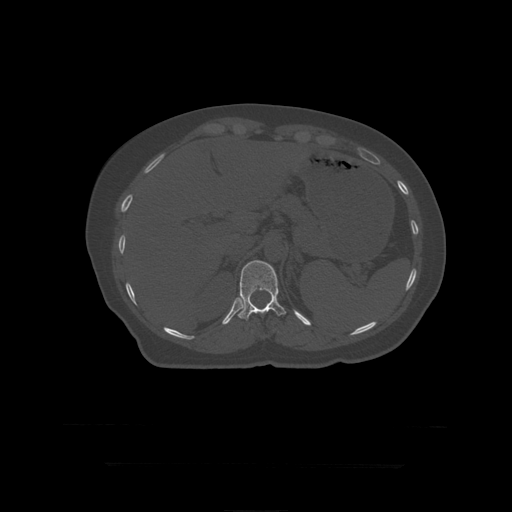
CT including the spine, one axial slice; reconstruction kernel STANDARD; 120 kVp; bone window (W 1800 / L 400 HU); 1.25 mm slice thickness; 512 × 512 image matrix. Patient age 41 years. From the clinical record (not read from this slice): primary cancer: breast.
Structures marked on this image (semi-automatic segmentation, software-assisted and operator-edited):
- T12 vertebra: box from (x=238, y=261) to (x=287, y=321) px